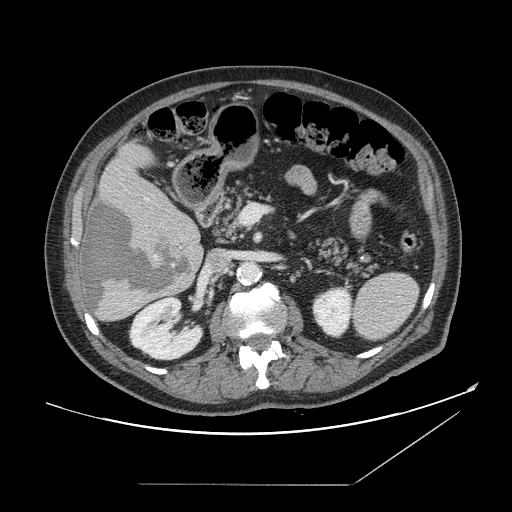
Contrast-enhanced abdominal CT, one axial slice; slice 76 of 166 in the series (ordered by position); intravenous contrast given; soft-tissue window (W 400 / L 40 HU); 512 × 512 image matrix, field of view 416 × 416 mm. Male patient, age 80 years. From the clinical record (not read from this slice): diagnosis: colorectal cancer liver metastases, imaged before liver resection; multiple liver metastases: no; largest metastasis: 2.2 cm.
Annotated regions visible in this slice (manually delineated by an expert):
- hepatic veins: box from (x=146, y=199) to (x=149, y=201) px
- liver: (x=80, y=145)–(x=204, y=323)
- planned liver remnant (the part of the liver to remain after resection): (x=102, y=144)–(x=196, y=229)
- liver metastasis: (x=84, y=194)–(x=194, y=313)